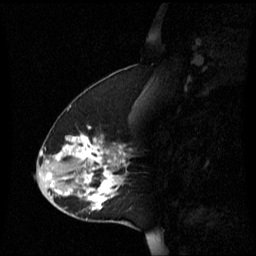
Breast MRI (dynamic contrast-enhanced), one sagittal slice; position 24 of 60 along the scan axis; dynamic contrast-enhanced series, image 2 of 3 at this slice position (ordered by acquisition); 1.5 T; TE 4.2 ms, TR 8.4 ms; 2.2 mm slice thickness; 256 × 256 image matrix. Patient: female, 45 years. From the clinical record (not read from this slice): setting: breast cancer imaged before/during neoadjuvant chemotherapy; receptor status: HR-positive, HER2-negative.
Structures marked on this image (semi-automatic segmentation, software-assisted and operator-edited):
- analysis volume of interest (the breast-tissue region the enhancement analysis was run in; not a lesion): bounding box (x1, y1, x2, y2) in pixels: (38, 126, 131, 221)
- tumour enhancement mask (voxels above the 70 % enhancement threshold inside the analysis volume of interest): (46, 128, 125, 211)